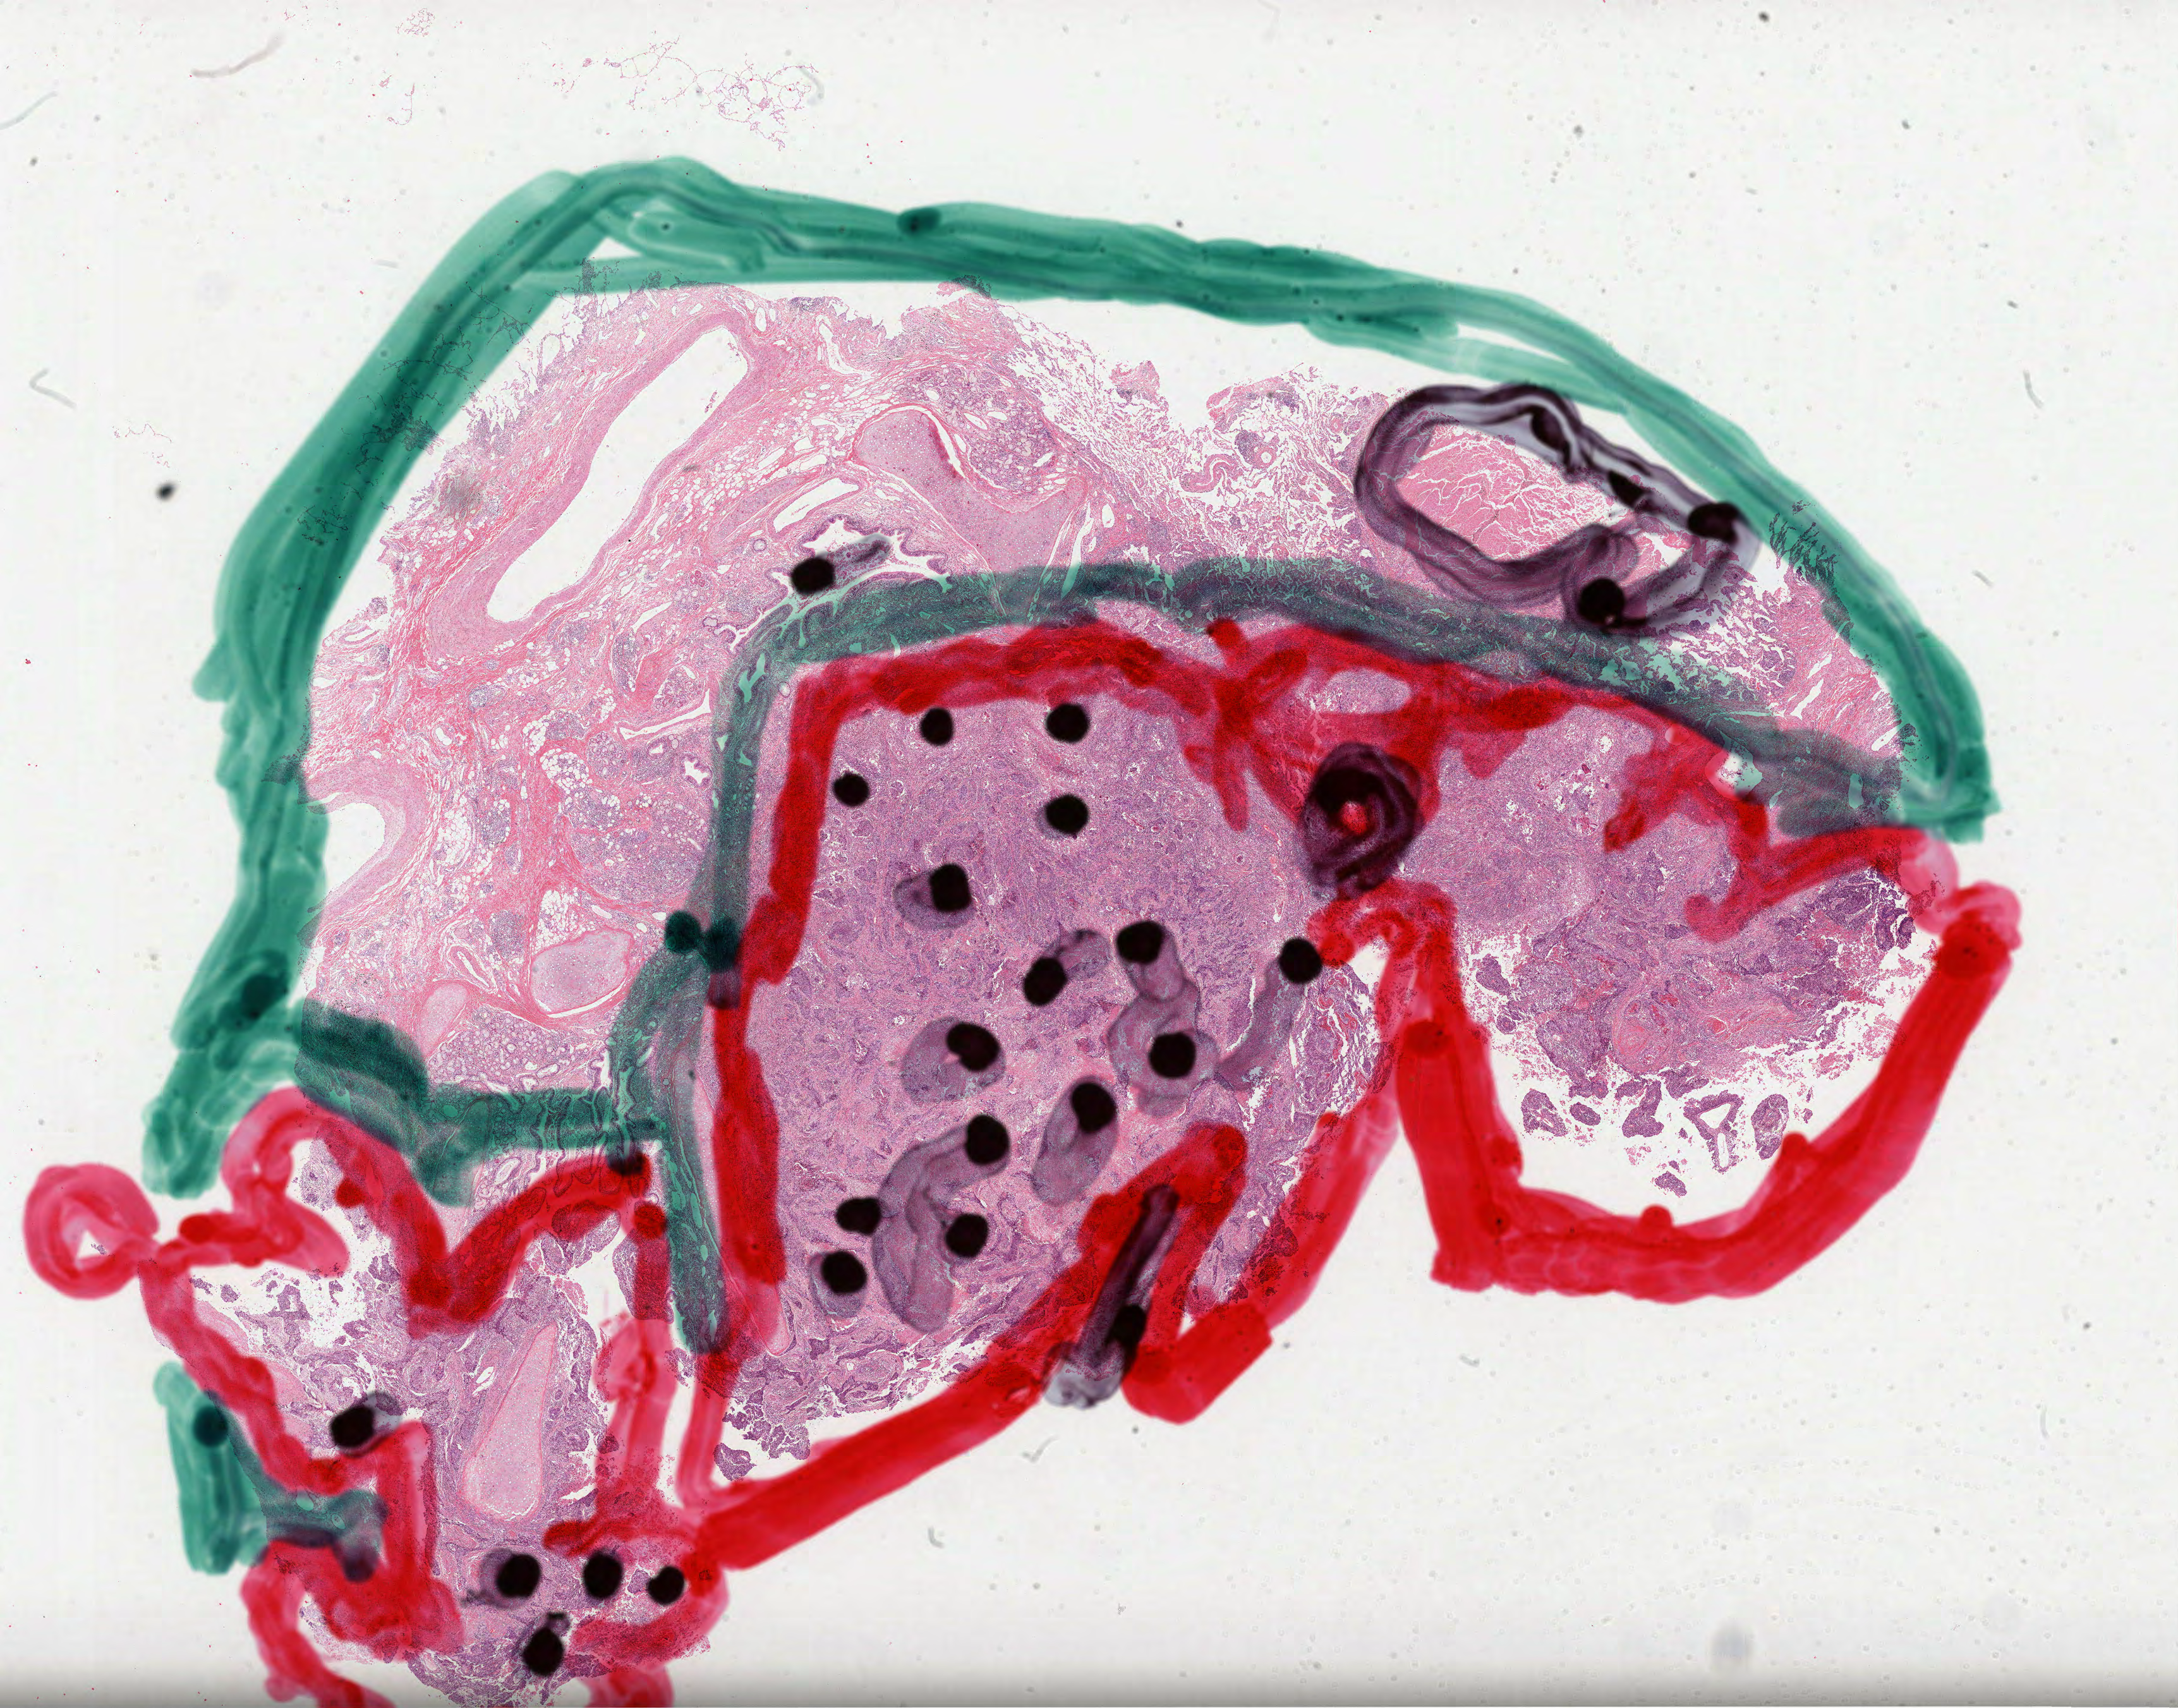
H&E whole-slide image, whole scanned area (about 27.8 x 21.8 mm, acquisition: 40x scan) shown as a low-resolution overview, FFPE section, sample: primary tumour, lung. Male, age 62 years at initial diagnosis.
Diagnosis: Squamous cell carcinoma, NOS (upper lobe, lung). Laterality: left. AJCC pathologic stage: IIA.